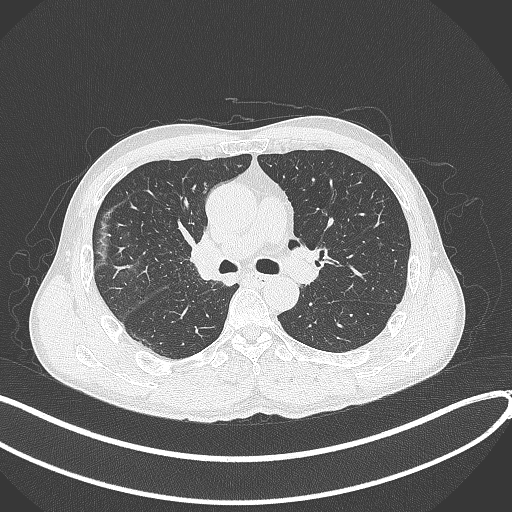
Chest CT, one axial slice. Position 235 of 409 along the scan axis. Reconstruction kernel B70f. Lung window (W 1500 / L -600 HU). 1 mm slice thickness. 512 × 512 image matrix, field of view 400 × 400 mm. Male patient, age 53 years. From the clinical record (not read from this slice): clinical TNM (as recorded): T1b N0 M0.
Structures marked on this image (bounding box drawn by a radiologist):
- lung tumour (recorded histology: squamous cell carcinoma): bounding box (x1, y1, x2, y2) in pixels: (184, 231, 223, 284)